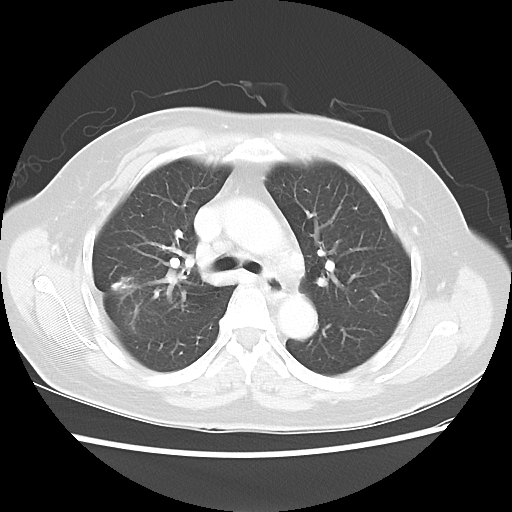
Chest CT, one axial slice; slice 23 of 40 in the series (ordered by position); 100 kVp; lung window (W 1500 / L -600 HU); 512 × 512 image matrix. Patient: female, 67 years. From the clinical record (not read from this slice): clinical TNM (as recorded): T1c N1 M0.
Outlined on this slice (bounding box drawn by a radiologist):
- lung tumour (recorded histology: adenocarcinoma): bounding box [x1, y1, x2, y2] px = [105, 269, 148, 299]